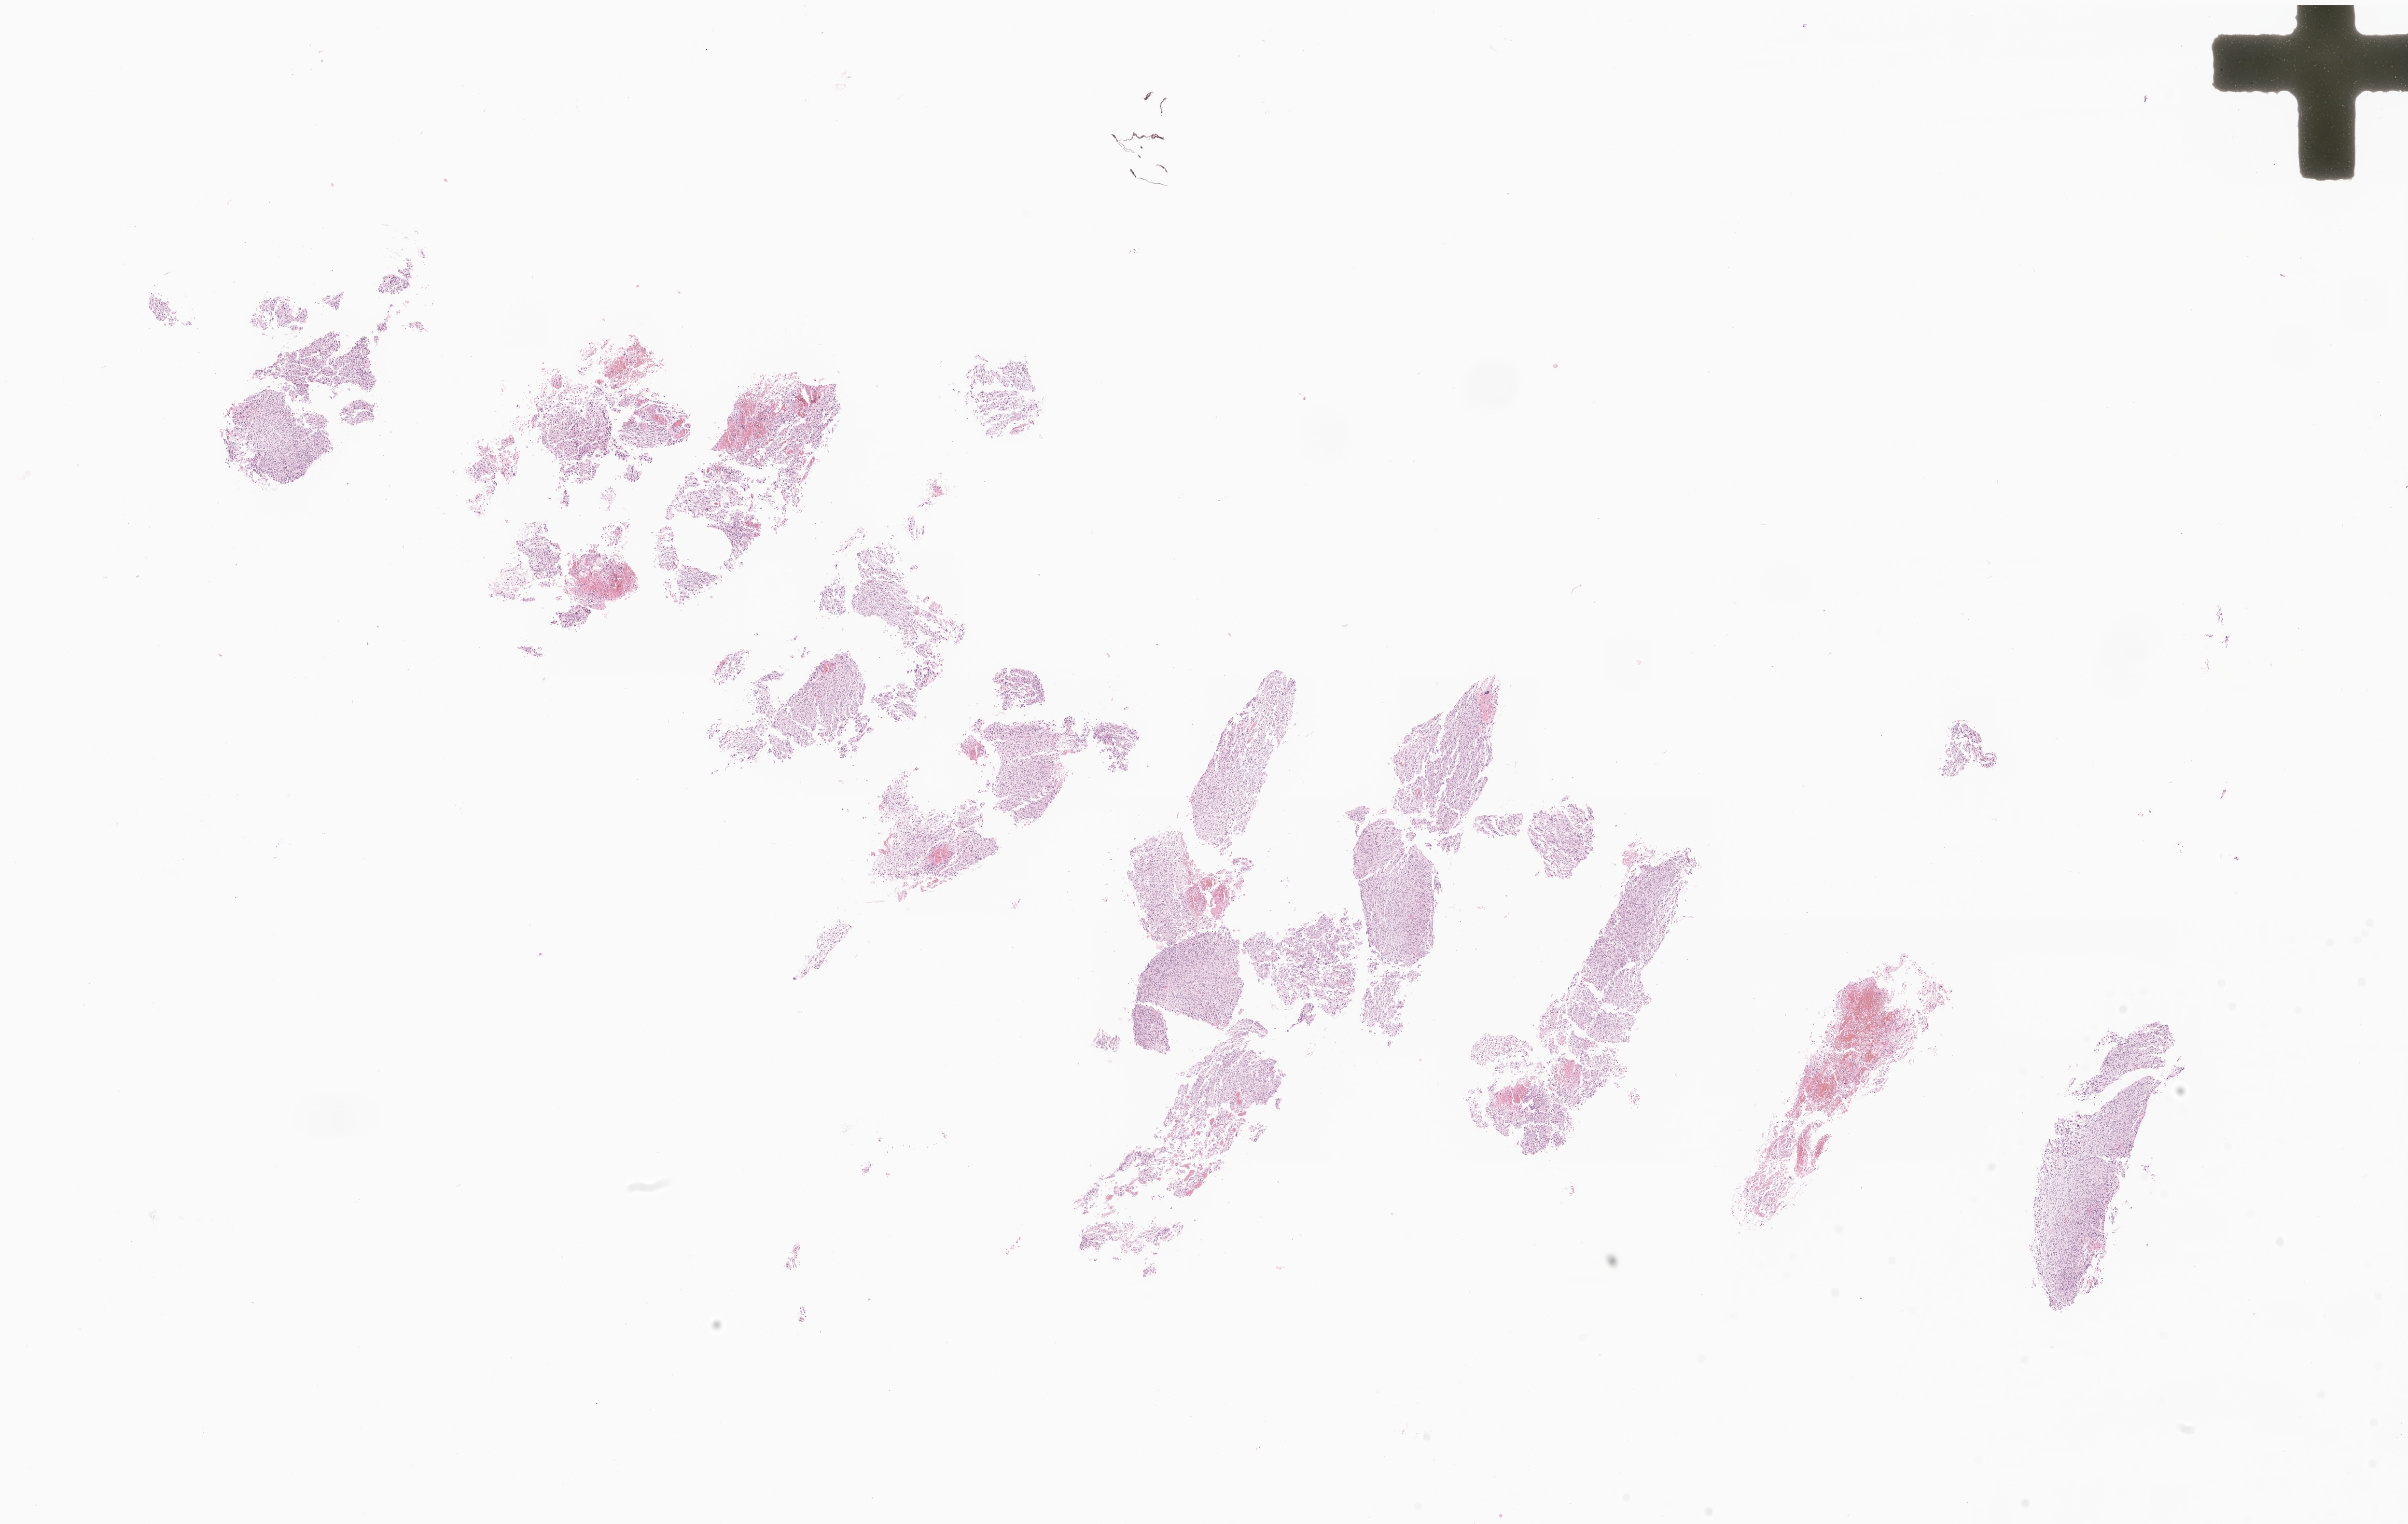
Whole-slide image, hematoxylin and eosin (H&E) stain of tumor tissue from the brain — low-resolution overview of the scanned area, about 21.0 x 13.3 mm, formalin-fixed paraffin-embedded section. Patient male; age 161 months (13 years 5 months).
• recorded diagnosis: Glioma, malignant